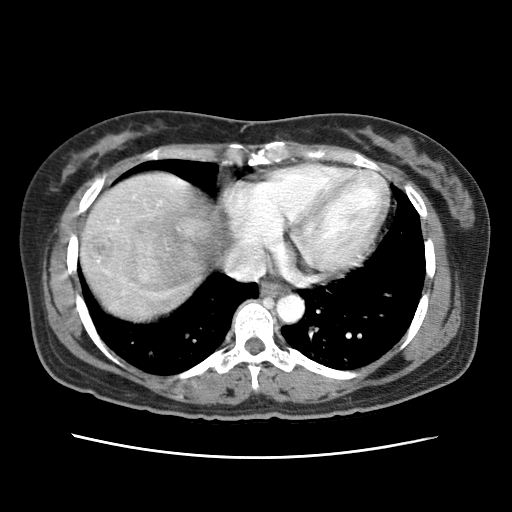
Contrast-enhanced abdominal CT (liver protocol), one axial slice. Slice 63 of 79 in the series (ordered by position). Soft-tissue window (W 400 / L 40 HU). 512 × 512 image matrix. Case-level facts recorded for this patient, not image findings: diagnosis: hepatocellular carcinoma (patient treated with transarterial chemoembolisation; whether this scan precedes or follows treatment is not stated here); TNM stage (as recorded): Stage-I; Child-Pugh class: A; tumour differentiation: moderately differentiated.
Outlined on this slice (semi-automatically segmented with operator editing):
- abdominal aorta: bounding box <276,294,303,322> (left, top, right, bottom; pixels)
- liver parenchyma outside the tumour (the mass and vessels are separate outlines, so this box may not span the whole liver): <80,172,210,320>
- mass: <125,214,216,292>
- liver vessels: <97,177,185,262>